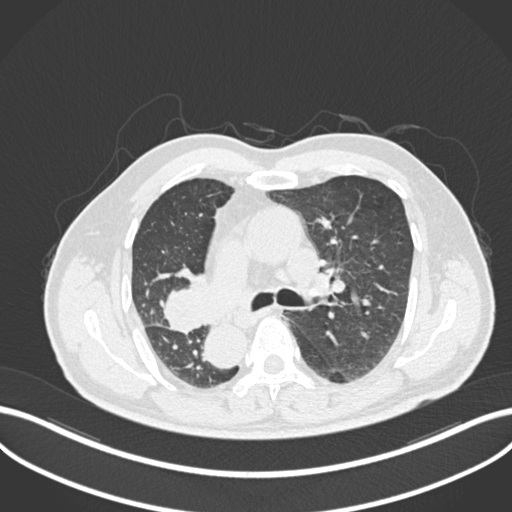
Chest CT, one axial slice; slice 146 of 206 in the series (ordered by position); reconstruction kernel B30f; 120 kVp; lung window (W 1500 / L -600 HU); 1 mm slice thickness; 512 × 512 image matrix, field of view 400 × 400 mm. Male patient, age 67 years. From the clinical record (not read from this slice): clinical TNM (as recorded): T2a N0 M0.
Outlined on this slice (bounding box drawn by a radiologist):
- lung tumour (recorded histology: squamous cell carcinoma): bounding box <157,270,211,337> (left, top, right, bottom; pixels)